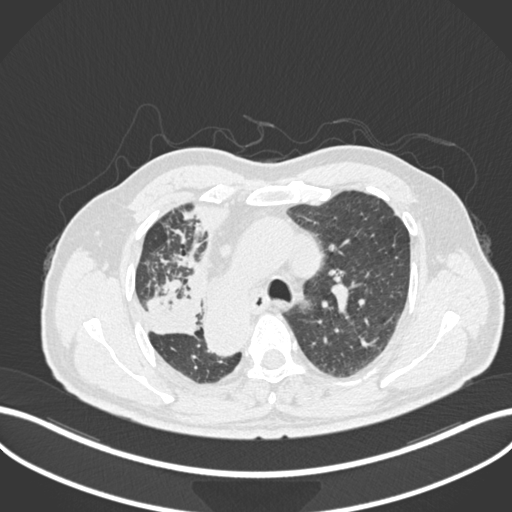
Chest CT, one axial slice. Slice 168 of 206 in the series (ordered by position). Lung window (W 1500 / L -600 HU). 1 mm slice thickness. 512 × 512 image matrix, field of view 400 × 400 mm. Patient: male, 67 years. From the clinical record (not read from this slice): clinical TNM (as recorded): T2a N0 M0.
Outlined on this slice (rectangle marked by the reading radiologist):
- lung tumour (recorded histology: squamous cell carcinoma): bounding box [x1, y1, x2, y2] px = [140, 274, 204, 337]